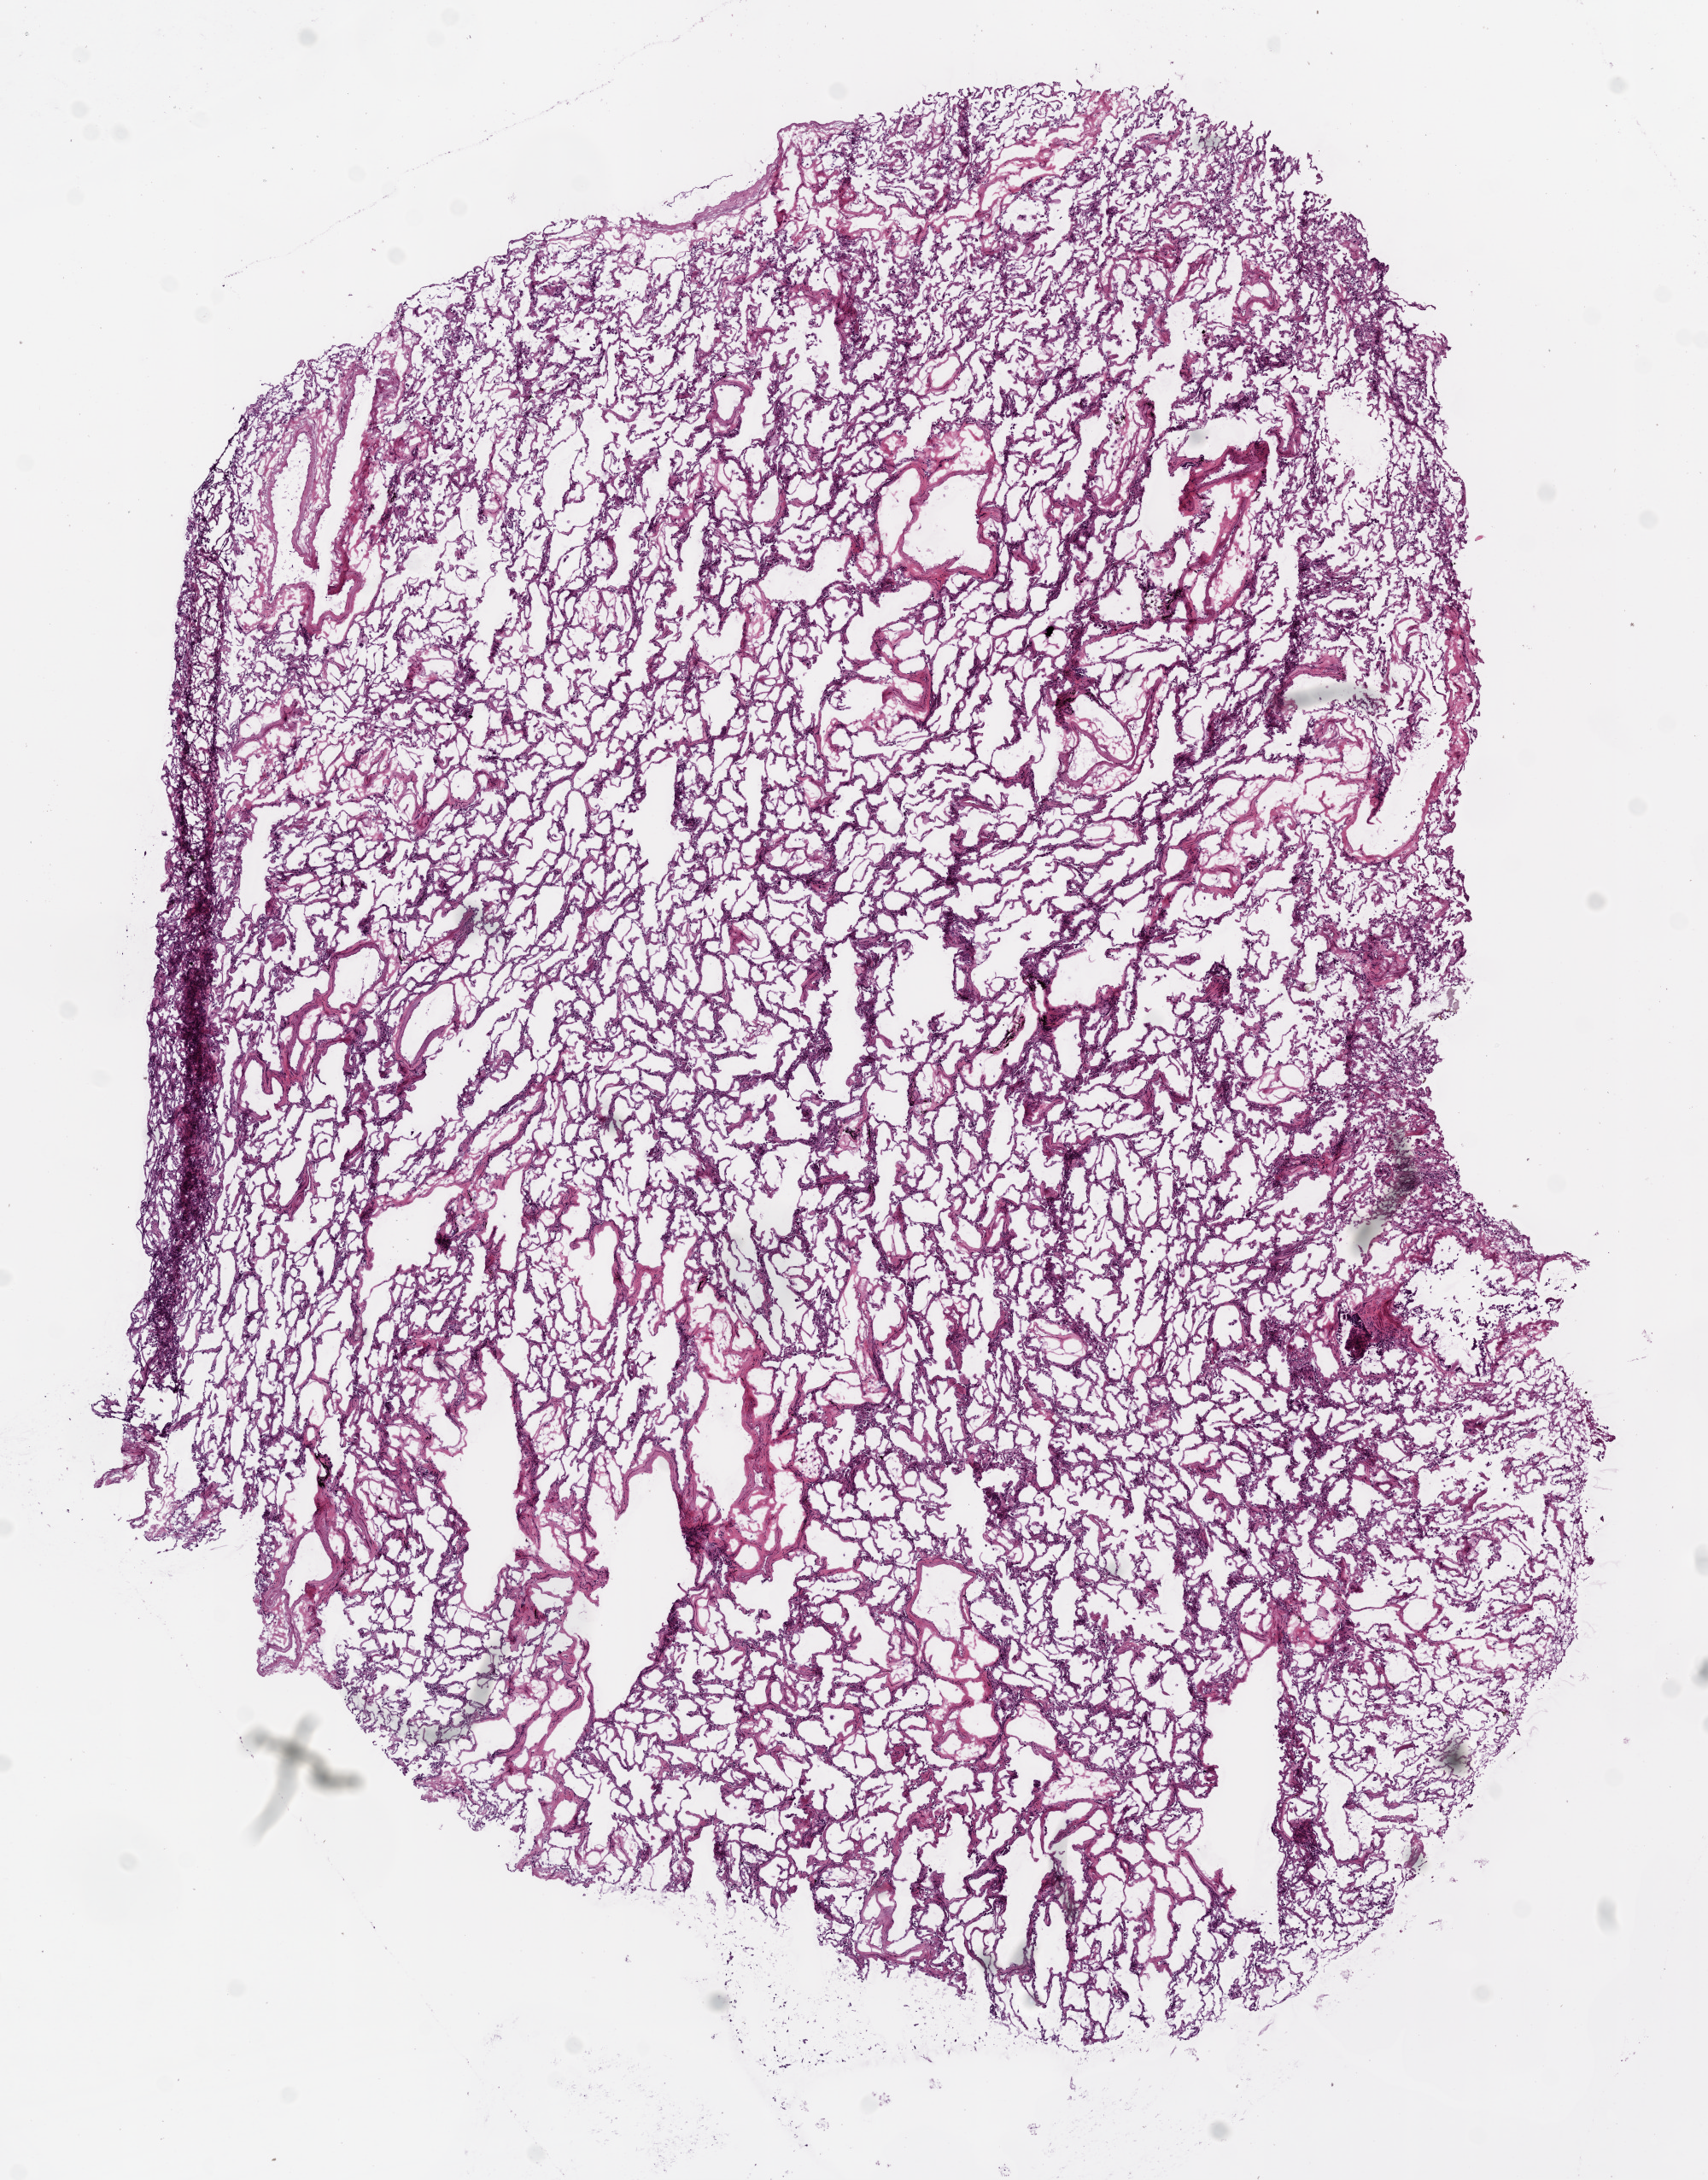
Hematoxylin and eosin (H&E) stained whole-slide image, a low-resolution overview of the entire scanned area, about 8.0 x 10.2 mm (slide scanned at 20x). Frozen section. Sample: solid tissue normal (non-tumour tissue), lung. Male, age 77 years at initial diagnosis.
• this section: solid tissue normal (non-tumour) sample from the same patient
• patient diagnosis: Adenocarcinoma, NOS (upper lobe, lung)